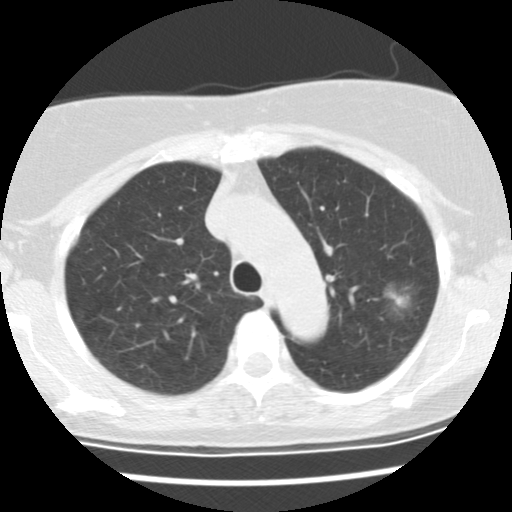
Low-dose screening chest CT, one axial slice. Position 104 of 137 along the scan axis. Reconstruction kernel STANDARD. 120 kVp. Lung window (W 1500 / L -600 HU). 512 × 512 image matrix, field of view 288 × 288 mm.
Outlined on this slice (expert manual segmentation):
- lesion 1 (tumor, upper lobe of left lung): bounding box [x1, y1, x2, y2] px = [385, 291, 410, 309]